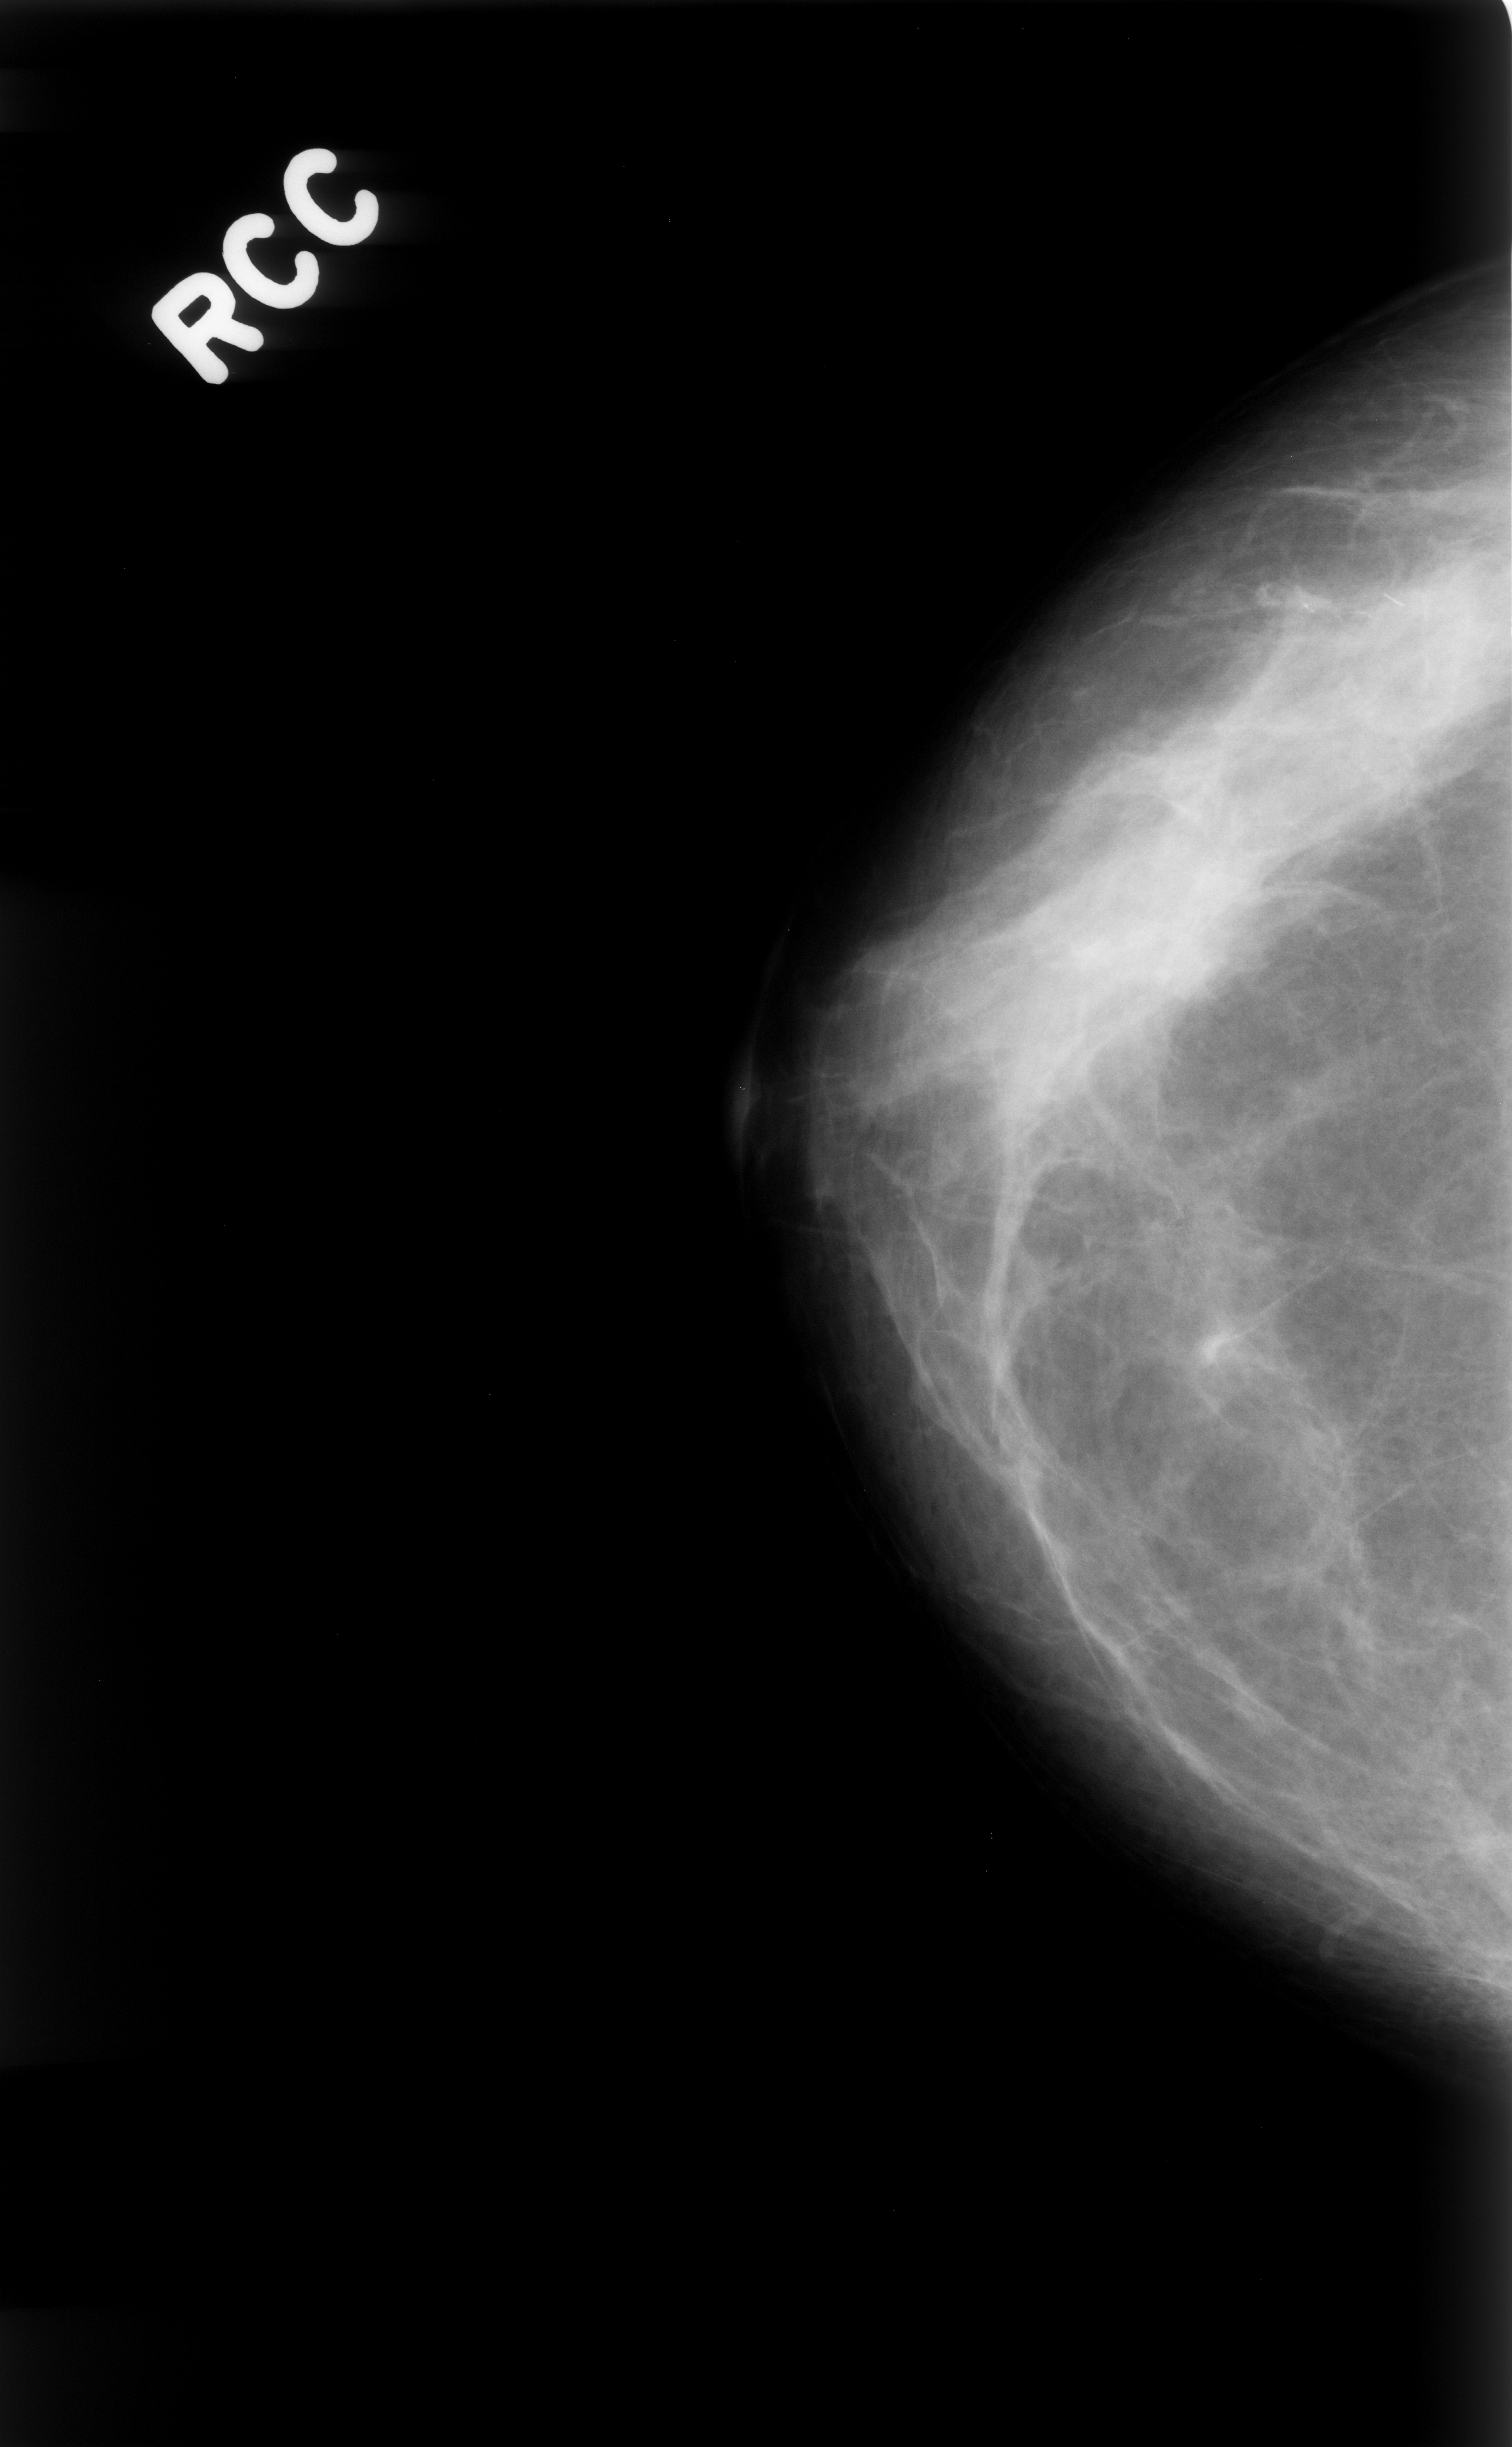
Digitized screen-film mammogram. Right breast. Craniocaudal (CC) view. 1512 × 2447 image matrix.
Marked abnormalities (boxes around the expert regions of interest):
- calcifications, morphology fine linear branching, distribution linear; BI-RADS assessment category 4; subtlety rating 4 on a 1 (subtle) to 5 (obvious) scale; pathology (as recorded): benign: box from (x=1176, y=452) to (x=1414, y=759) px